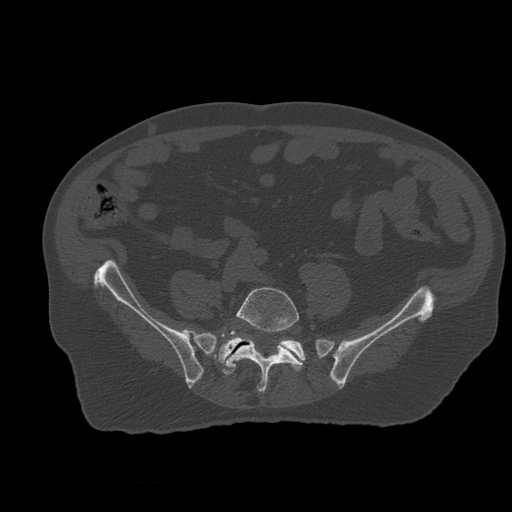
CT including the spine, one axial slice. Position 137 of 399 along the scan axis. Reconstruction kernel STANDARD. Bone window (W 1800 / L 400 HU). 1.25 mm slice thickness. 512 × 512 image matrix, field of view 407 × 407 mm. Patient age 73 years. Case-level facts recorded for this patient, not image findings: primary cancer: prostate; vertebrae with lytic lesions (as recorded): L2.
Outlined on this slice (semi-automatically segmented with operator editing):
- L5 vertebra: bounding box (x1, y1, x2, y2) in pixels: (222, 288, 303, 393)